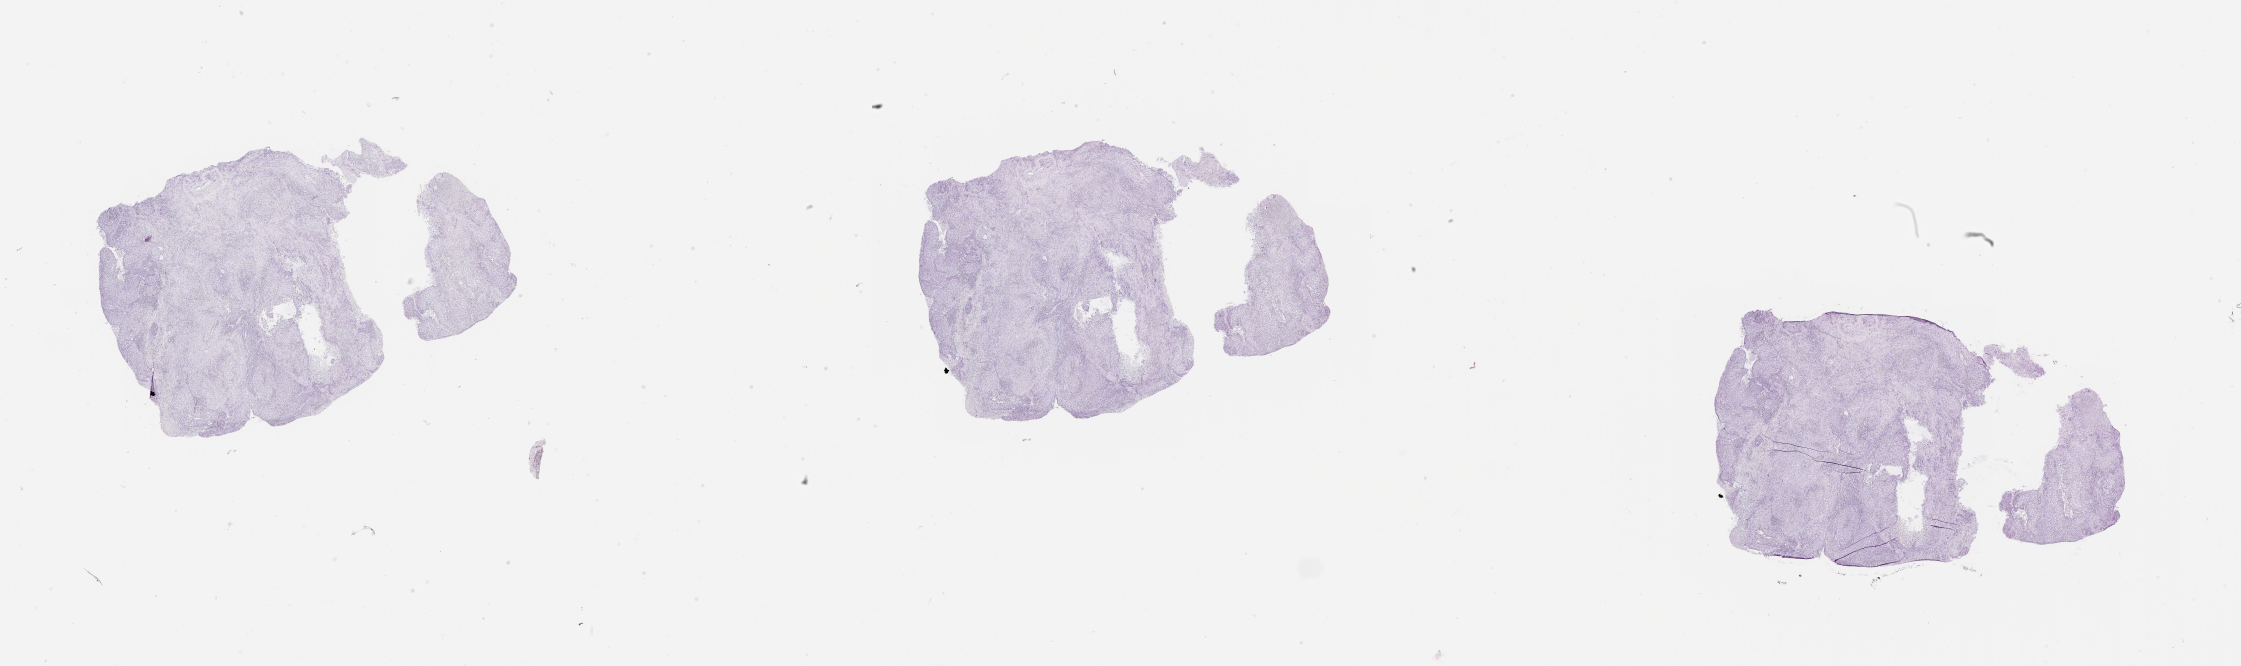
H&E whole-slide image, whole scanned area (about 36.1 x 10.7 mm, from a 20x scan) shown as a low-resolution overview, lung, tumour tissue. Patient: male, age 66 years.
Patient diagnosis (cohort enrolment): squamous cell carcinoma (lung).